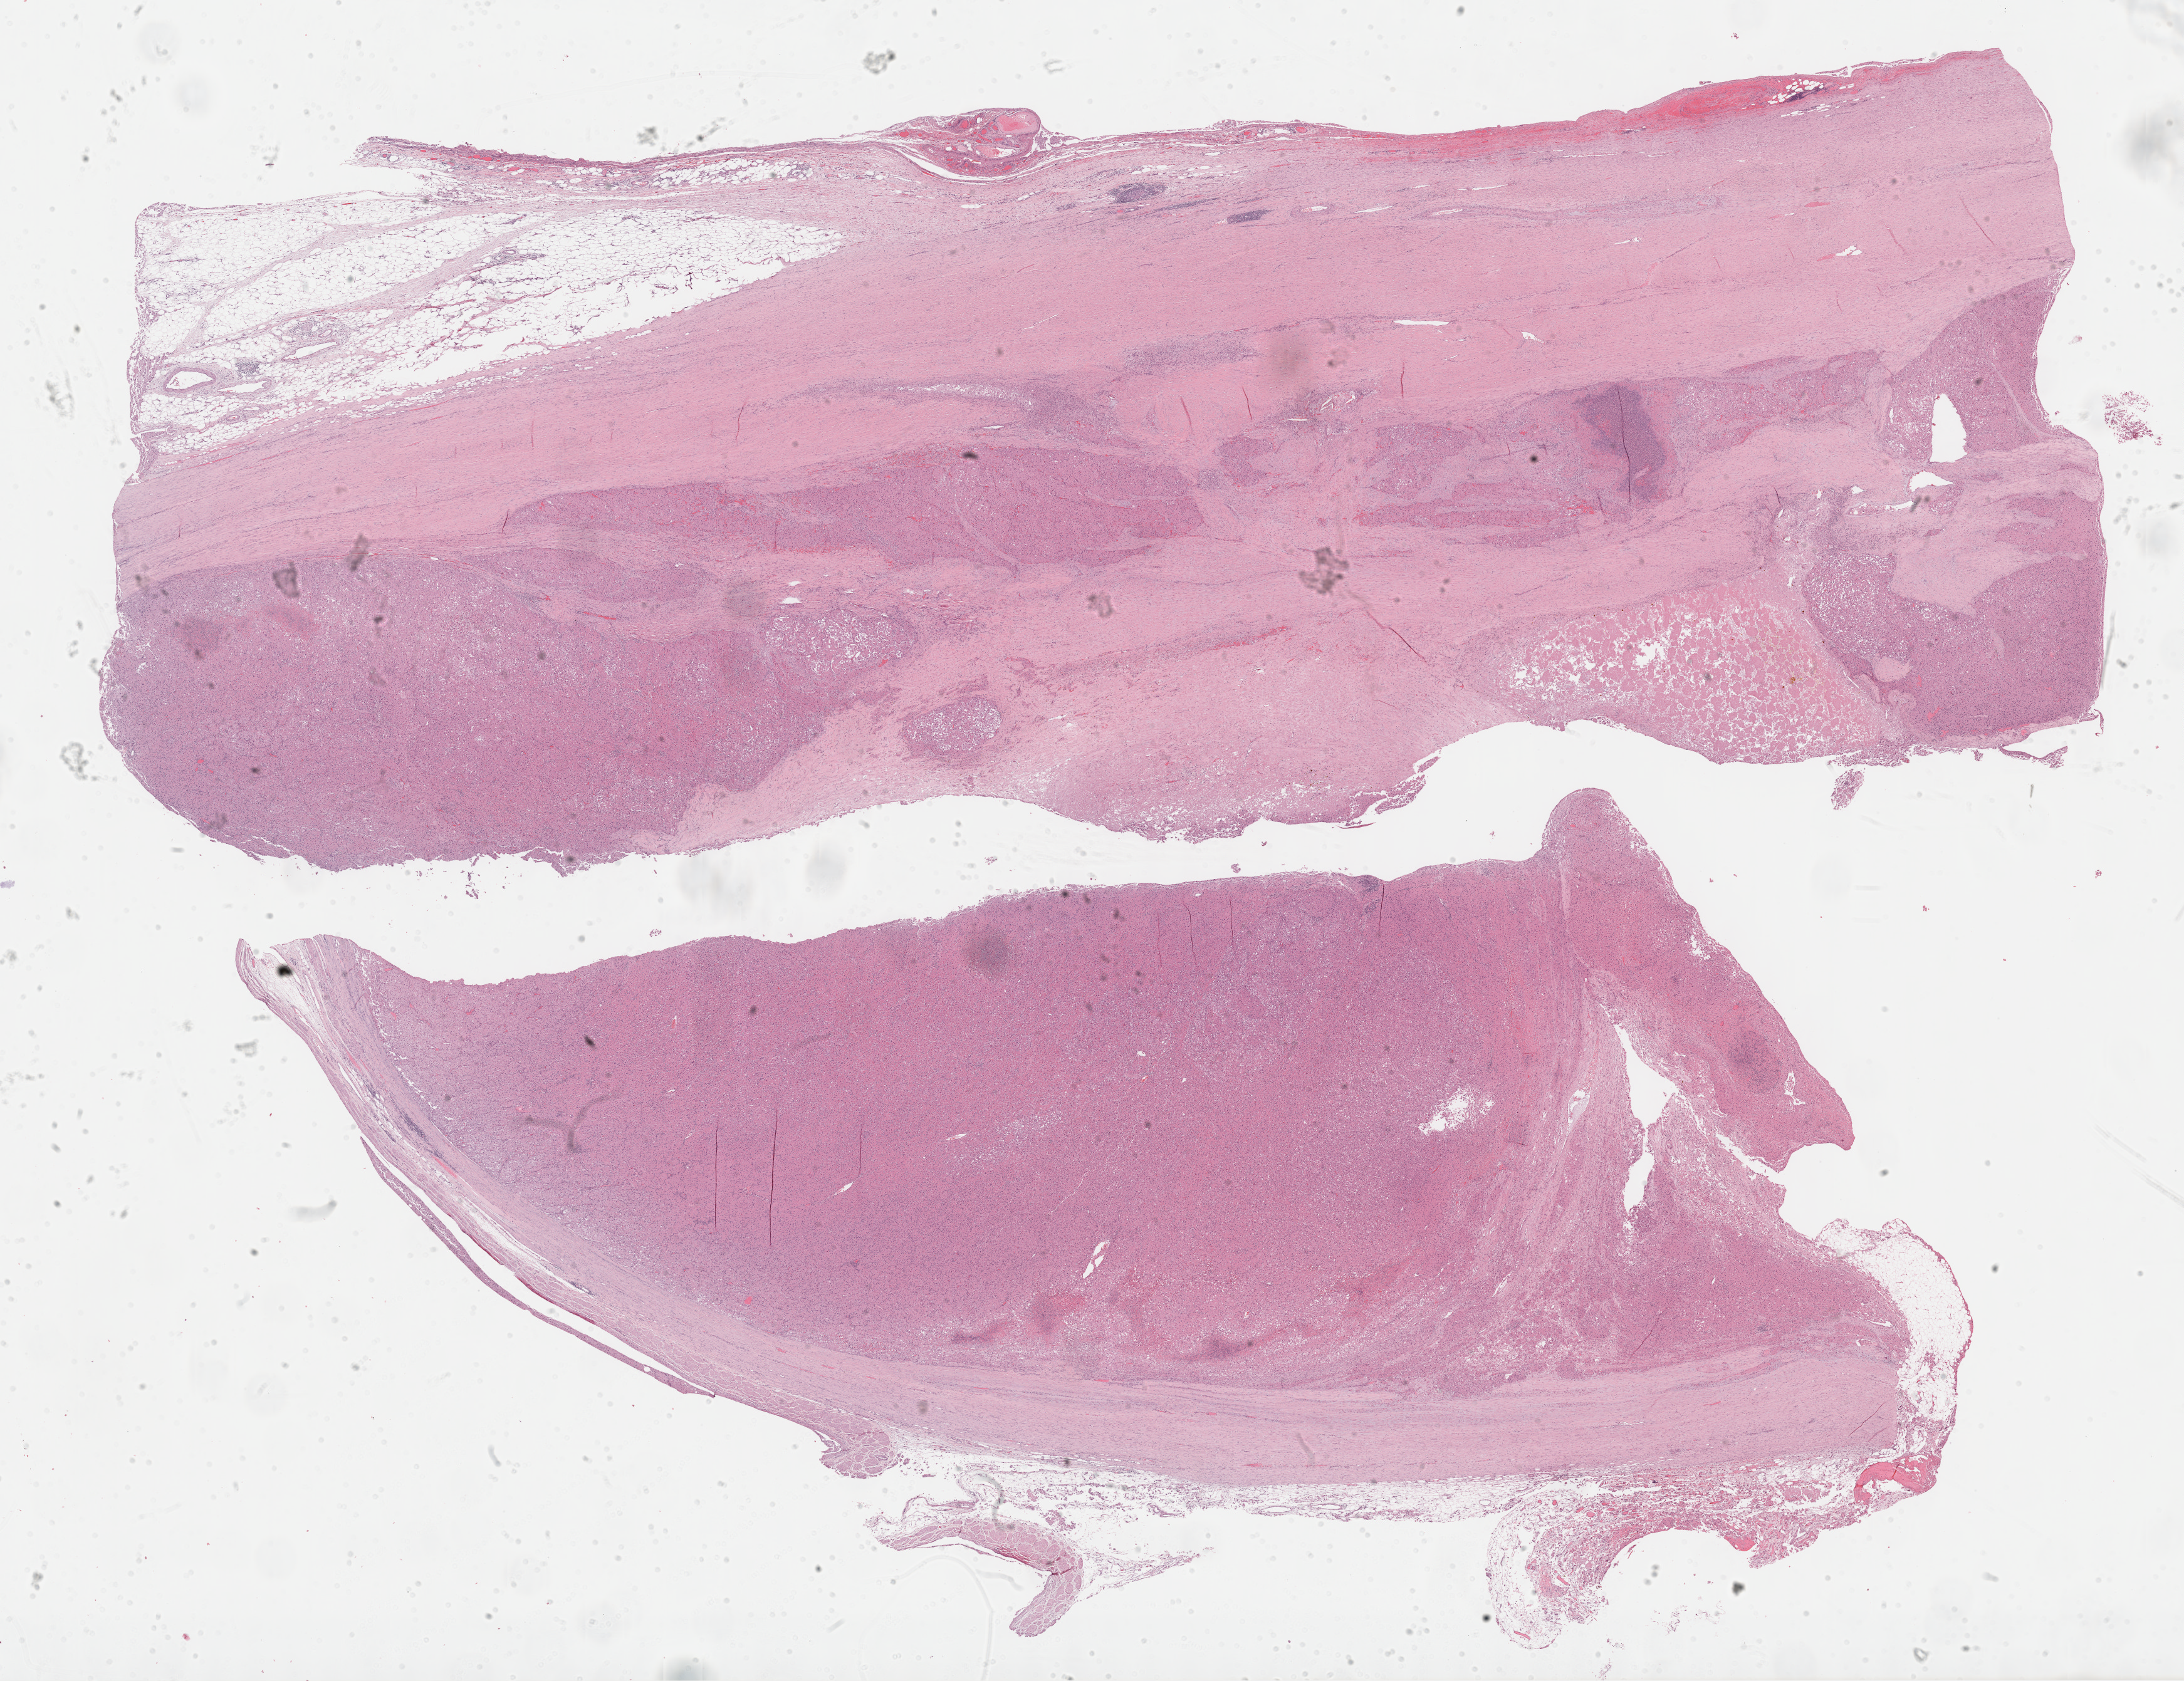
Whole-slide histology image, H&E-stained — a low-resolution overview of the entire scanned area, about 28.2 x 21.7 mm (acquisition: 40x scan), formalin-fixed paraffin-embedded (FFPE) diagnostic section, sample: primary tumour, adrenal cortex. Male patient; age at initial diagnosis 55 years.
- lymph nodes positive (case pathology): 0 of 1 examined
- laterality: left
- pathologic diagnosis: Adrenal cortical carcinoma